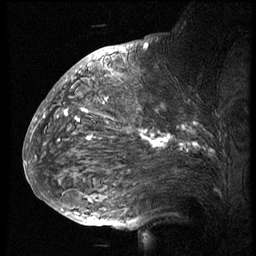
Breast MRI (dynamic contrast-enhanced), one sagittal slice; slice 43 of 74 in the series (ordered by position); 3 images stored at this slice position (order not interpretable as contrast timing); 1.5 T; TE 4.2 ms, TR 8.9 ms; 2.5 mm slice thickness; 256 × 256 image matrix, field of view 200 × 200 mm. Patient: female, 57 years. From the clinical record (not read from this slice): setting: breast cancer imaged before/during neoadjuvant chemotherapy; receptor status: HER2-positive.
Annotated regions visible in this slice (semi-automatic segmentation, software-assisted and operator-edited):
- analysis volume of interest (the breast-tissue region the enhancement analysis was run in; not a lesion): bounding box [x1, y1, x2, y2] px = [51, 67, 247, 173]
- tumour enhancement mask (voxels above the 140 % enhancement threshold inside the analysis volume of interest): [58, 99, 198, 151]